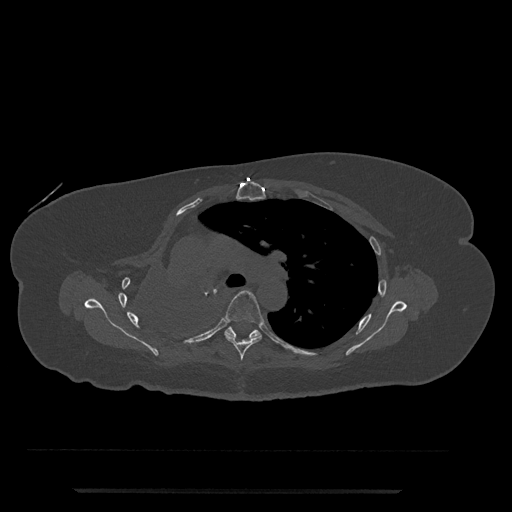
CT including the spine, one axial slice. Slice 527 of 797 in the series (ordered by position). Reconstruction kernel Br40s/3. Bone window (W 1800 / L 400 HU). 0.5 mm slice thickness. 512 × 512 image matrix, field of view 440 × 440 mm. Female patient, age 51 years. Case-level facts recorded for this patient, not image findings: primary cancer: neuro; vertebrae with lytic lesions (as recorded): T8.
Annotated regions visible in this slice (semi-automatically segmented with operator editing):
- T5 vertebra: bounding box (x1, y1, x2, y2) in pixels: (224, 290, 265, 361)
- T6 vertebra: (225, 327, 261, 339)